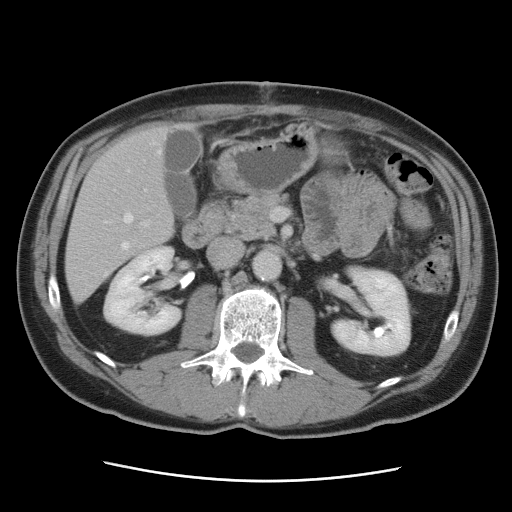
Contrast-enhanced abdominal CT, one axial slice; position 39 of 89 along the scan axis; intravenous contrast given; soft-tissue window (W 400 / L 40 HU); 5 mm slice thickness; 512 × 512 image matrix. Male patient, age 59 years. Case-level facts recorded for this patient, not image findings: diagnosis: colorectal cancer liver metastases, imaged before liver resection; multiple liver metastases: yes; largest metastasis: 0.6 cm; chemotherapy before resection: no.
Outlined on this slice (outlined manually by an expert reader):
- hepatic veins: box from (x=105, y=143) to (x=162, y=276) px
- liver: (x=66, y=125)–(x=174, y=303)
- planned liver remnant (the part of the liver to remain after resection): (x=74, y=125)–(x=174, y=245)
- portal vein (with intrahepatic branches): (x=142, y=190)–(x=149, y=226)